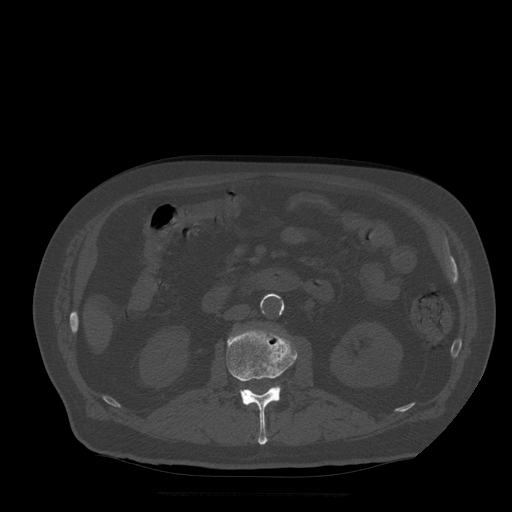
CT including the spine, one axial slice; position 164 of 522 along the scan axis; bone window (W 1800 / L 400 HU); 1.25 mm slice thickness; 512 × 512 image matrix, field of view 420 × 420 mm. Patient age 72 years. Case-level facts recorded for this patient, not image findings: primary cancer: prostate.
Outlined on this slice (semi-automatically segmented with operator editing):
- L2 vertebra: box from (x=227, y=330) to (x=298, y=445) px